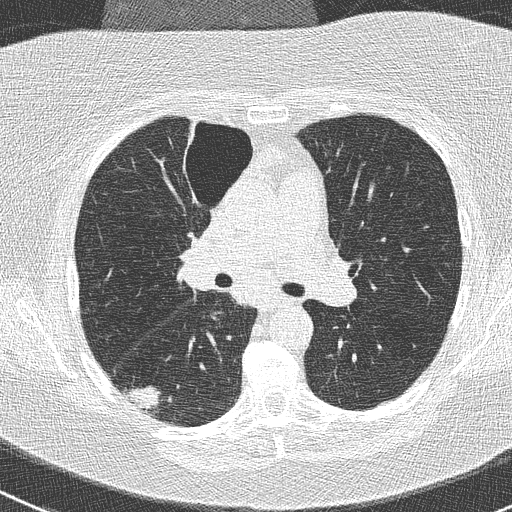
Low-dose screening chest CT, one axial slice. Slice 158 of 261 in the series (ordered by position). Reconstruction kernel B50f. 120 kVp. Lung window (W 1500 / L -600 HU). 2 mm slice thickness. 512 × 512 image matrix, field of view 310 × 310 mm.
Annotated regions visible in this slice (outlined manually by an expert reader):
- lesion 1 (tumor, lower lobe of right lung): bounding box (x1, y1, x2, y2) in pixels: (125, 386, 160, 411)